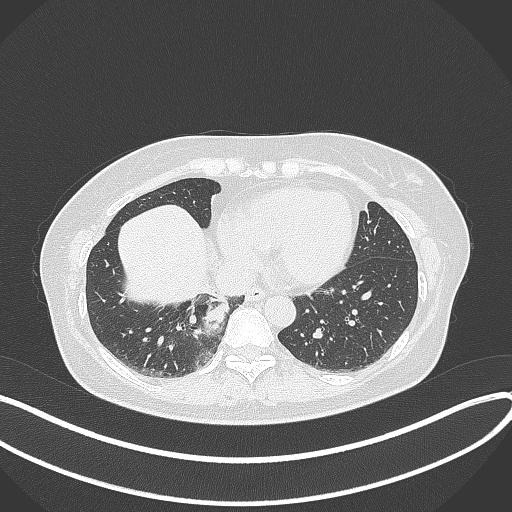
Chest CT, one axial slice. Position 106 of 331 along the scan axis. Reconstruction kernel B70f. Lung window (W 1500 / L -600 HU). 512 × 512 image matrix, field of view 400 × 400 mm. Patient: female, 54 years. Case-level facts recorded for this patient, not image findings: clinical TNM (as recorded): T4 N0 M0.
Structures marked on this image (bounding box drawn by a radiologist):
- lung tumour (recorded histology: adenocarcinoma): box from (x=201, y=292) to (x=233, y=339) px